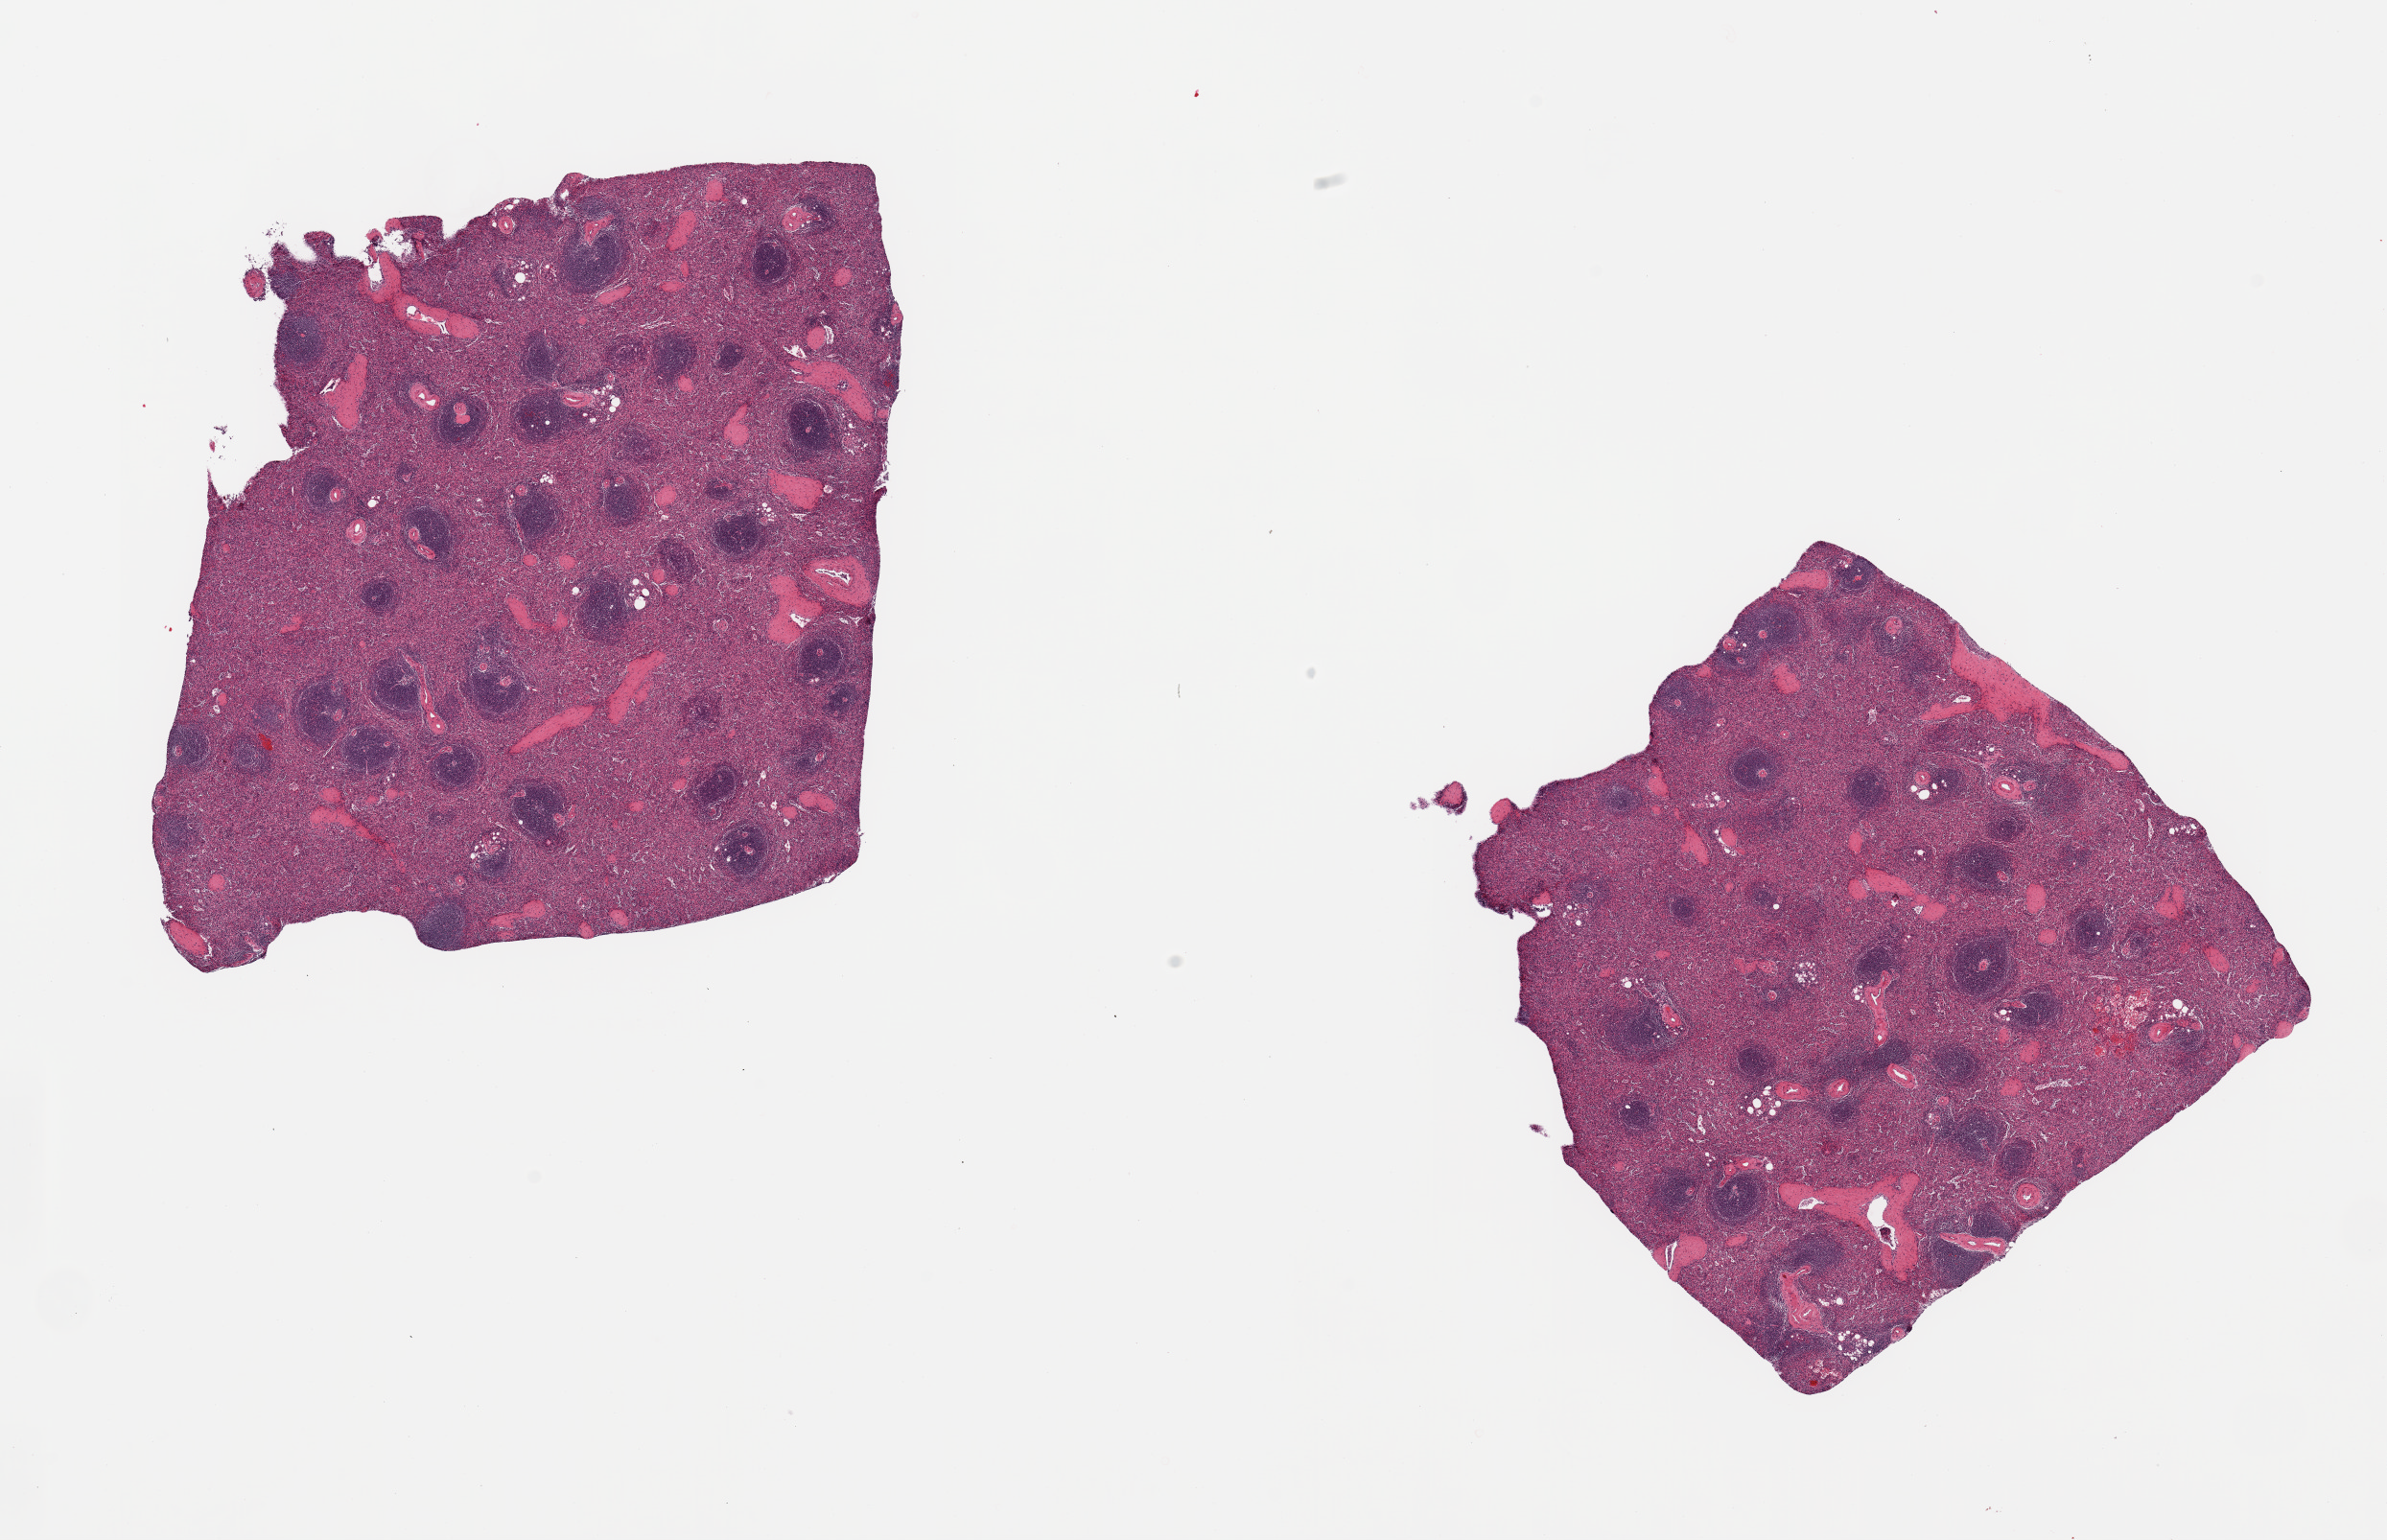
Digitized hematoxylin and eosin (H&E)-stained section, brightfield — low-resolution overview of the scanned area, about 19.7 x 12.7 mm (from a 20x scan), PAXgene-fixed, paraffin-embedded tissue, target tissue: spleen, tissue donor sample. Donor sex: female.
Reviewer comment on this tissue sample: 2 pieces; well preserved, non-congested.